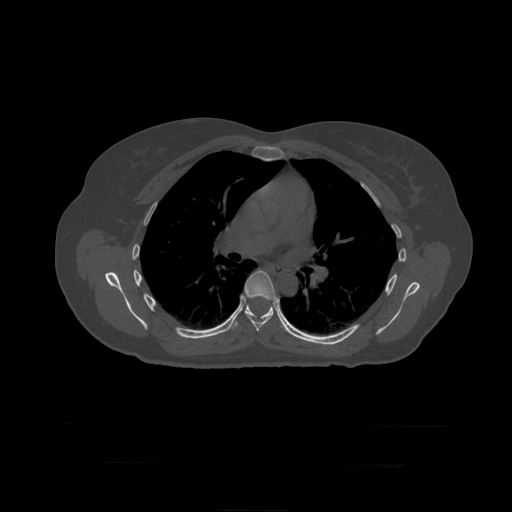
CT including the spine, one axial slice; position 294 of 399 along the scan axis; 120 kVp; bone window (W 1800 / L 400 HU); 1.25 mm slice thickness; 512 × 512 image matrix. Patient age 41 years. Case-level facts recorded for this patient, not image findings: primary cancer: breast.
Annotated regions visible in this slice (semi-automatically segmented with operator editing):
- T7 vertebra: bounding box <241,271,277,331> (left, top, right, bottom; pixels)
- T8 vertebra: <231,305,275,329>